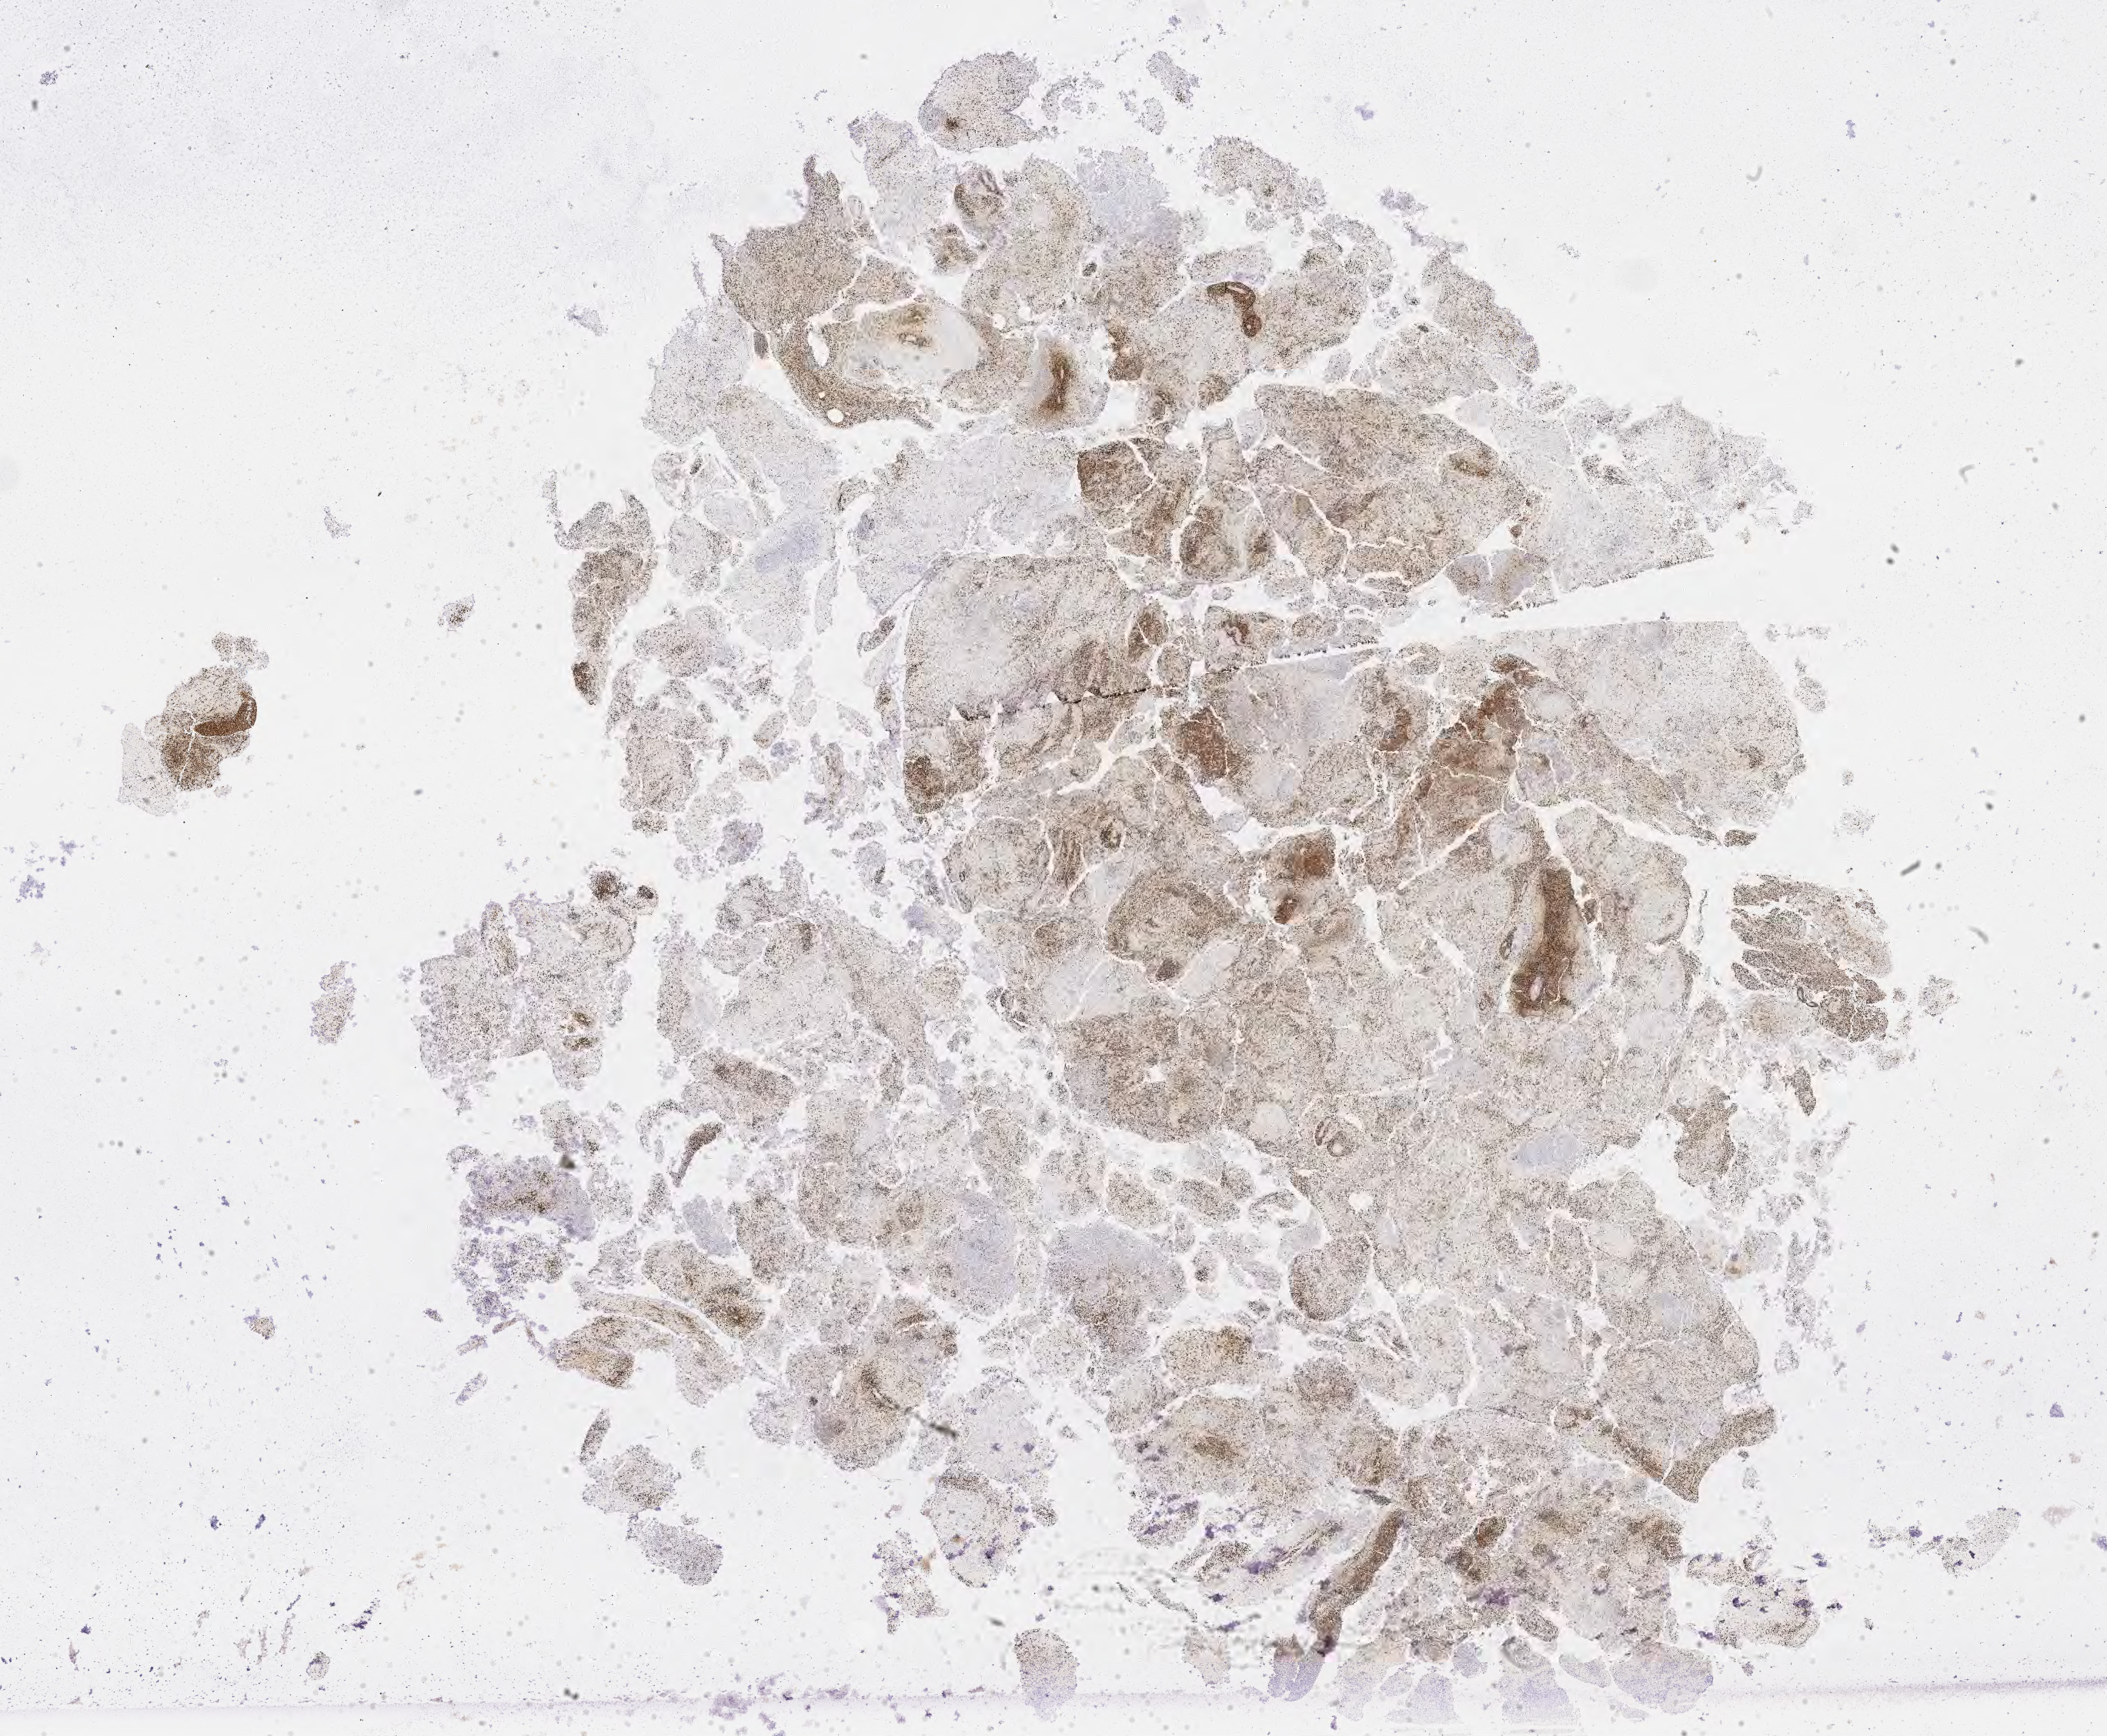
Whole-slide image, Epstein–Barr virus-encoded RNA (EBER) in-situ hybridisation, low-resolution overview of the scanned area, about 22.1 x 18.2 mm; tumor tissue; site: brain. Patient male; aged 51.
• diagnosis: Diffuse large B-cell lymphoma, NOS